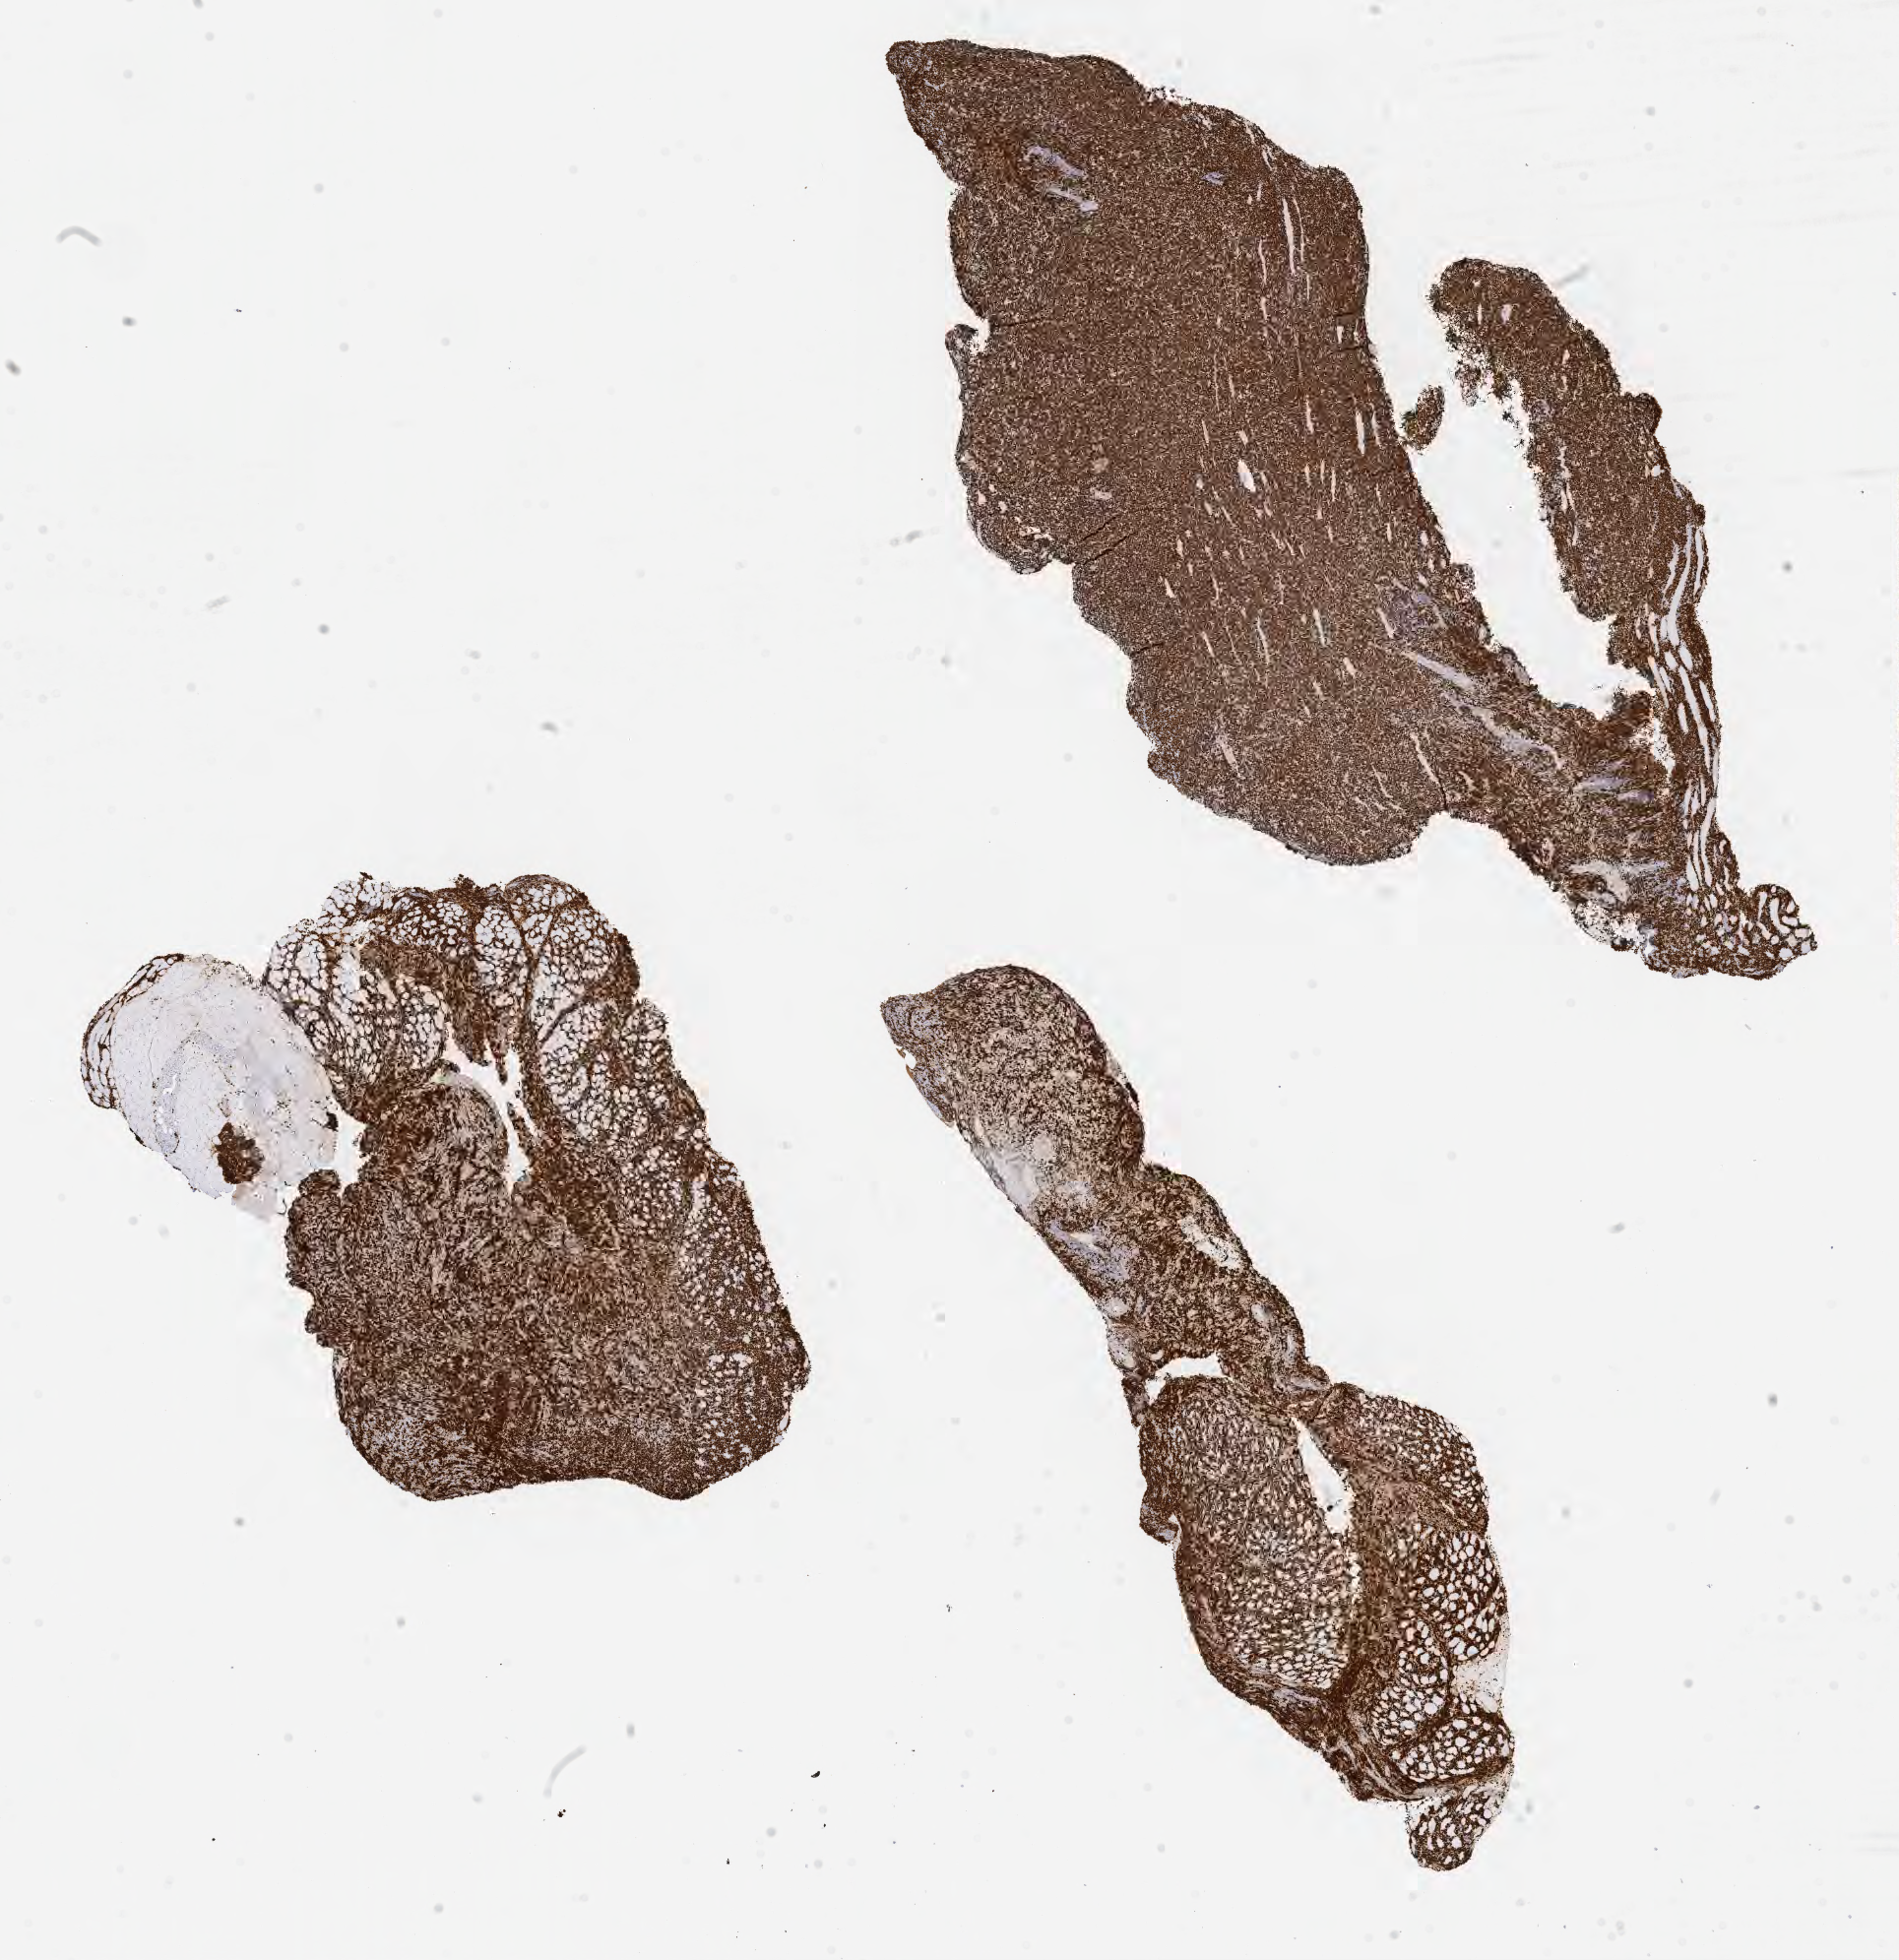
Whole-slide image, immunohistochemical stain for Ki-67, low-resolution overview of the scanned area, about 15.6 x 16.1 mm, specimen: tumor tissue, anatomic site: lymph node of head and neck. Male patient, 55 years old.
Diagnosis: Burkitt lymphoma, NOS.